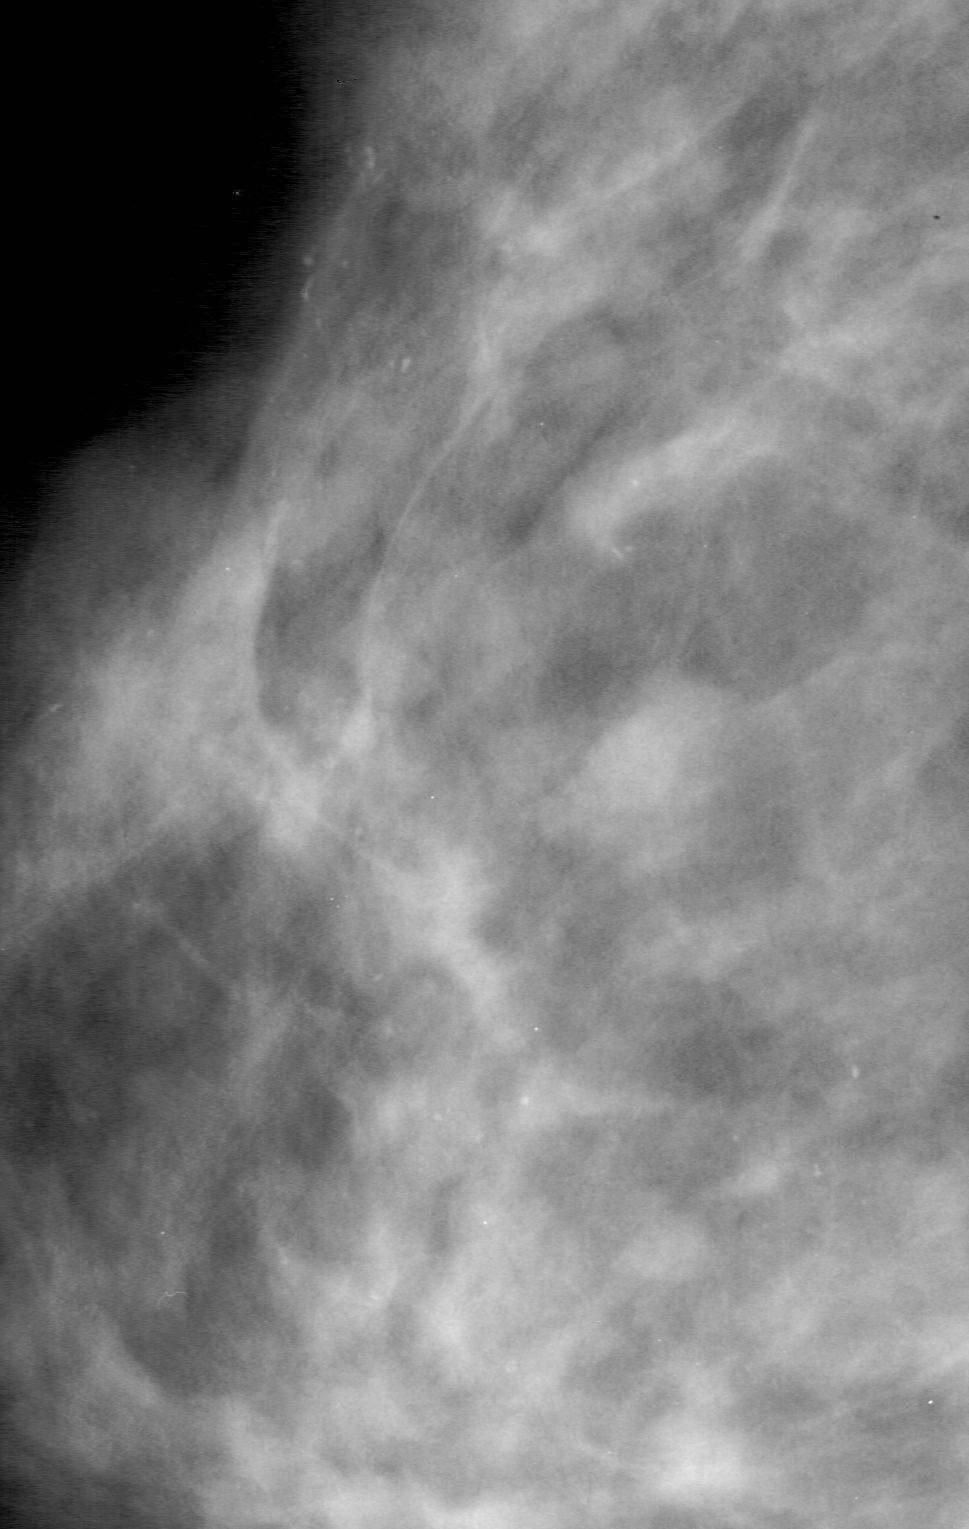
Region of interest cut from a scanned film mammogram (one marked finding); left breast; MLO view.
Calcifications, morphology pleomorphic, distribution segmental; BI-RADS assessment category 4; subtlety rating 3 on a 1 (subtle) to 5 (obvious) scale; pathology result (as recorded, not read from the image): malignant.